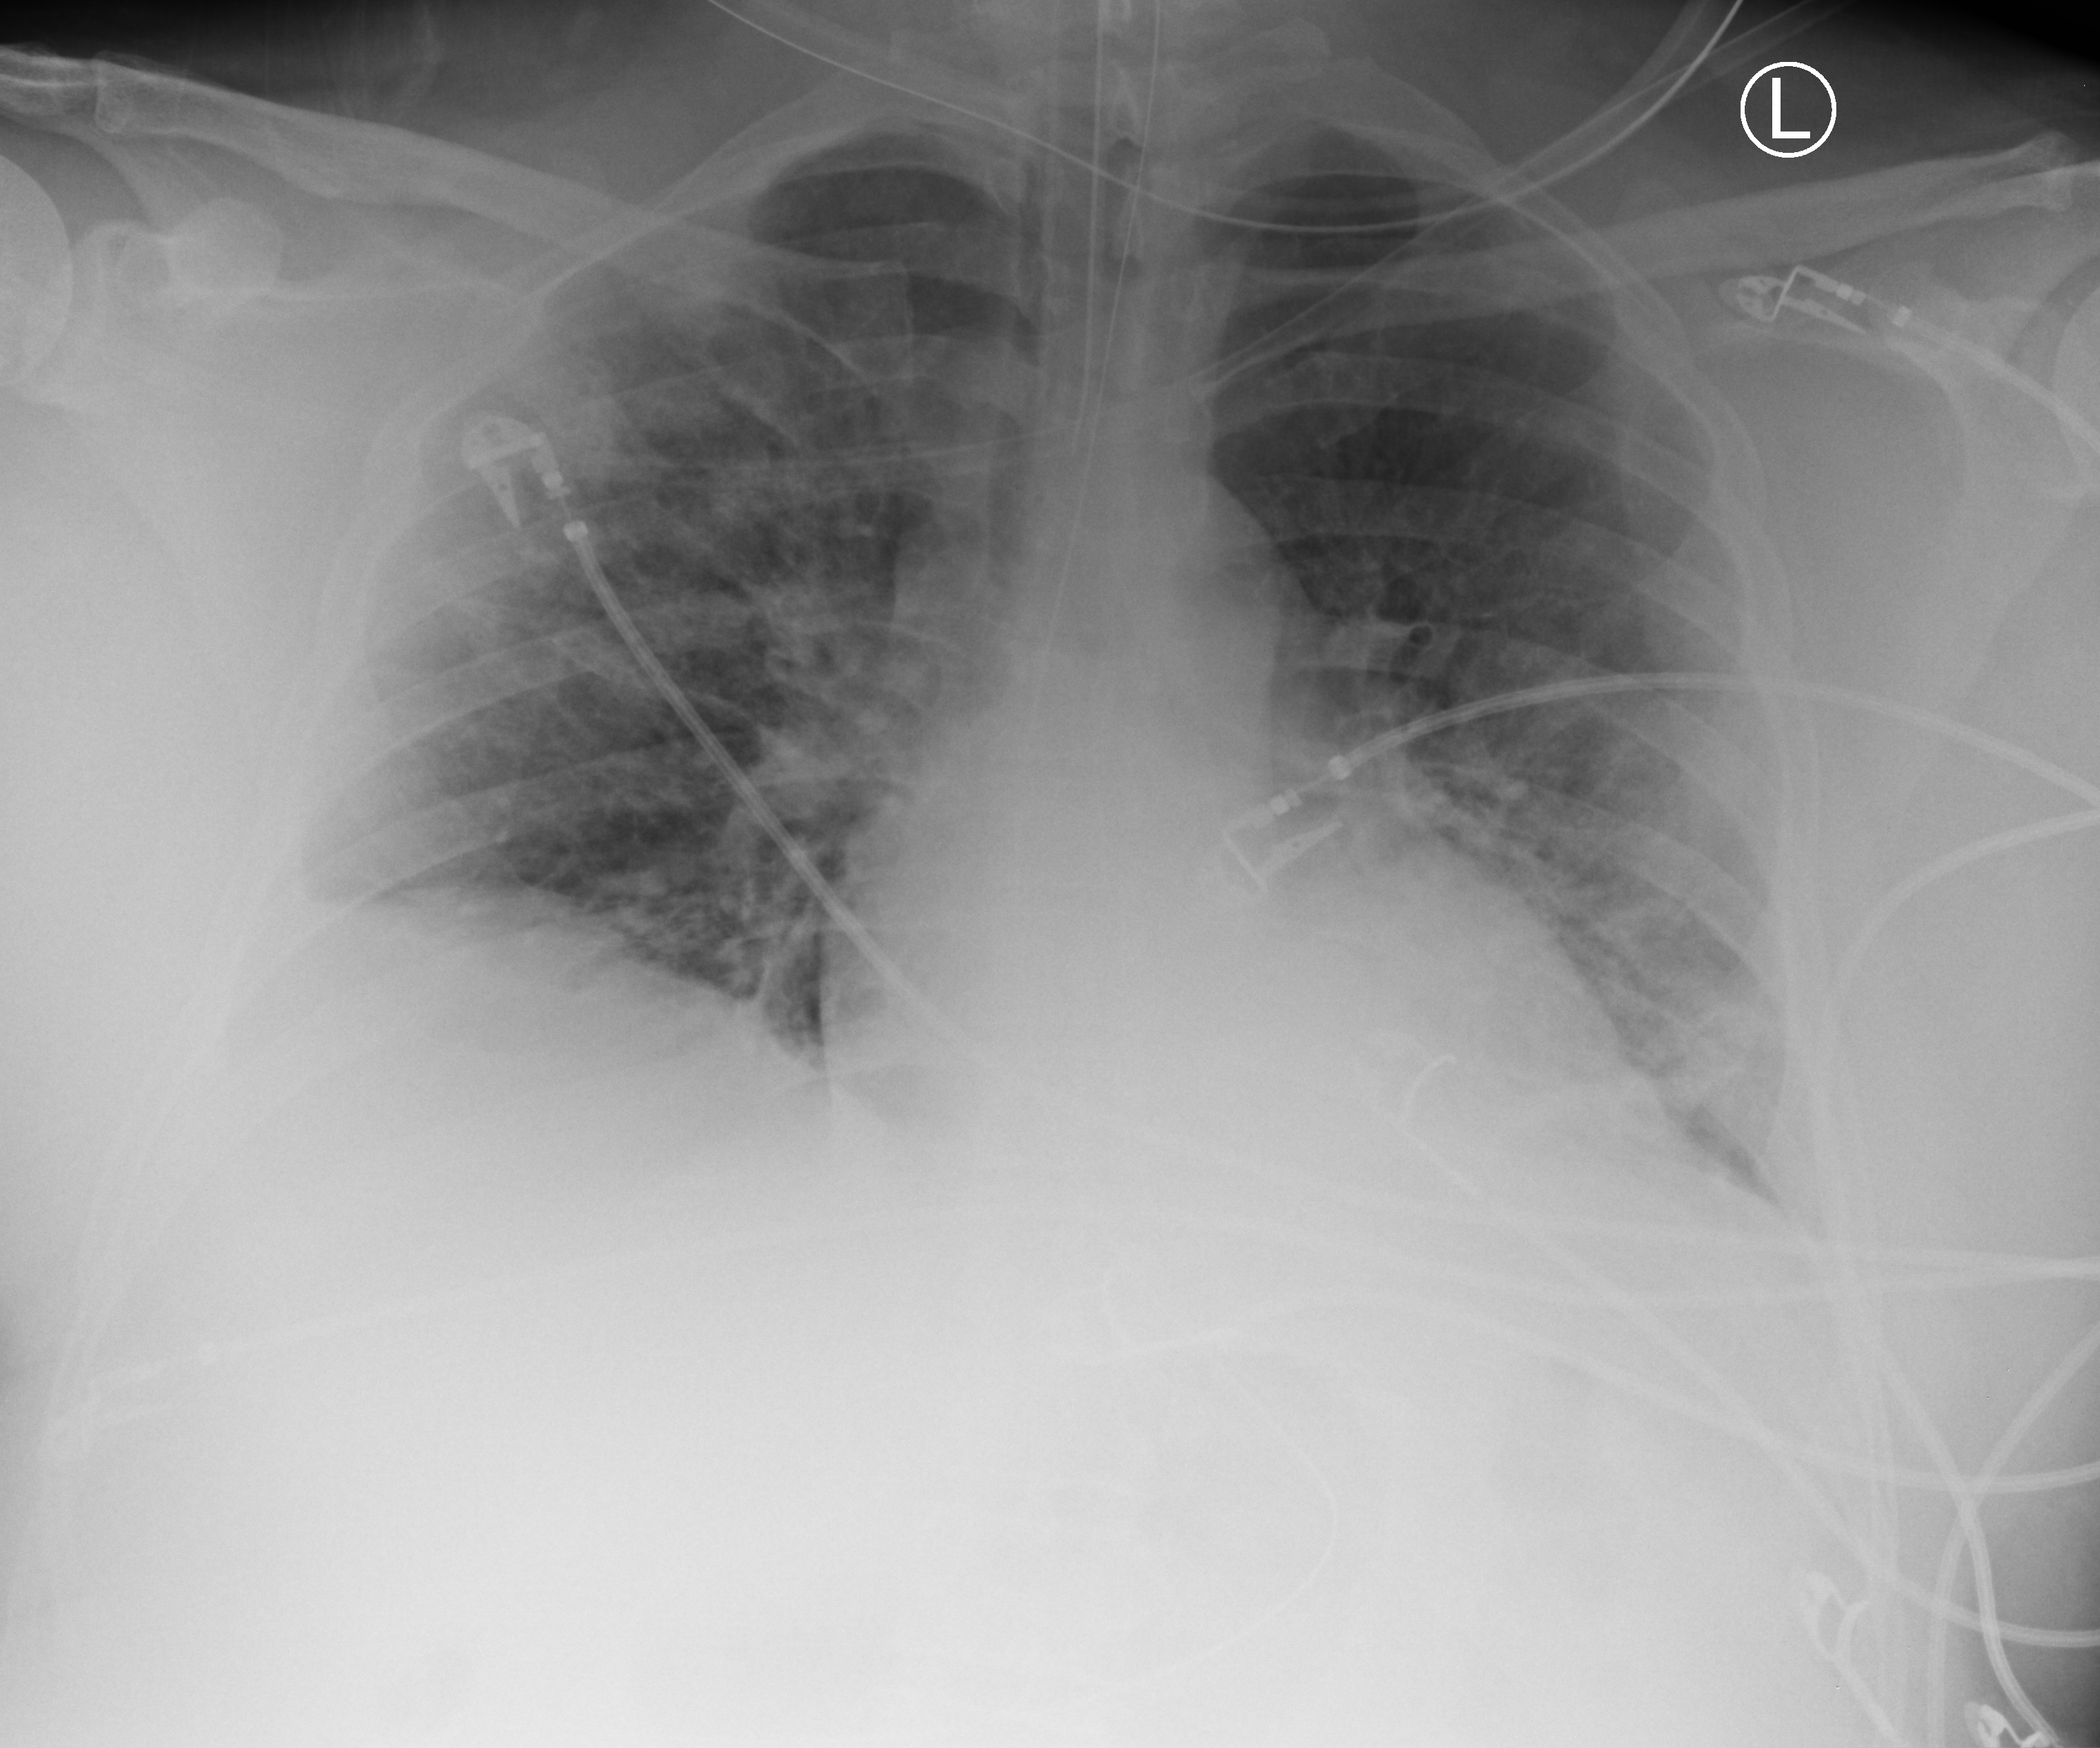
Bedside chest radiograph (computed radiography). Adult patient hospitalised with COVID-19, age 18–59 years.
Hospital-stay facts (about this admission, not read from this image; timing relative to this image not recorded): admitted to intensive care during this hospital stay: yes; other chronic lung disease (admission record): yes.